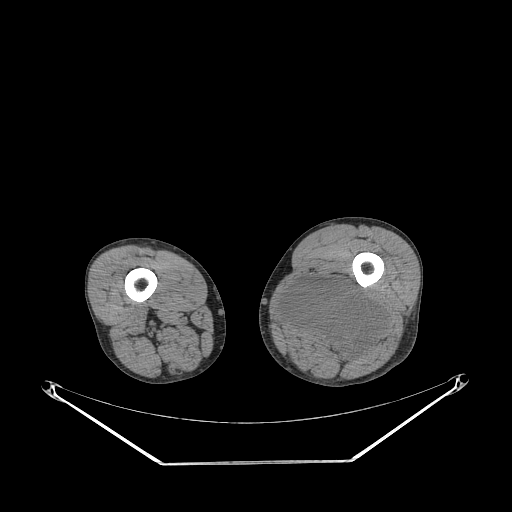
CT of an extremity soft-tissue mass (from a PET/CT study), one axial slice. Slice 222 of 267 in the series (ordered by position). Reconstruction kernel STANDARD. 140 kVp. Soft-tissue window (W 400 / L 40 HU). 3.75 mm slice thickness. 512 × 512 image matrix, field of view 500 × 500 mm. Male patient. From the clinical record (not read from this slice): histological type: undifferentiated pleomorphic liposarcoma; grade: high; site of the primary tumour: left thigh.
Annotated regions visible in this slice (expert contour drawn on MRI and transferred to this co-registered scan by the dataset authors):
- gross tumour volume including surrounding oedema: bounding box [x1, y1, x2, y2] px = [281, 278, 385, 360]
- gross tumour volume (mass): [281, 278, 385, 360]